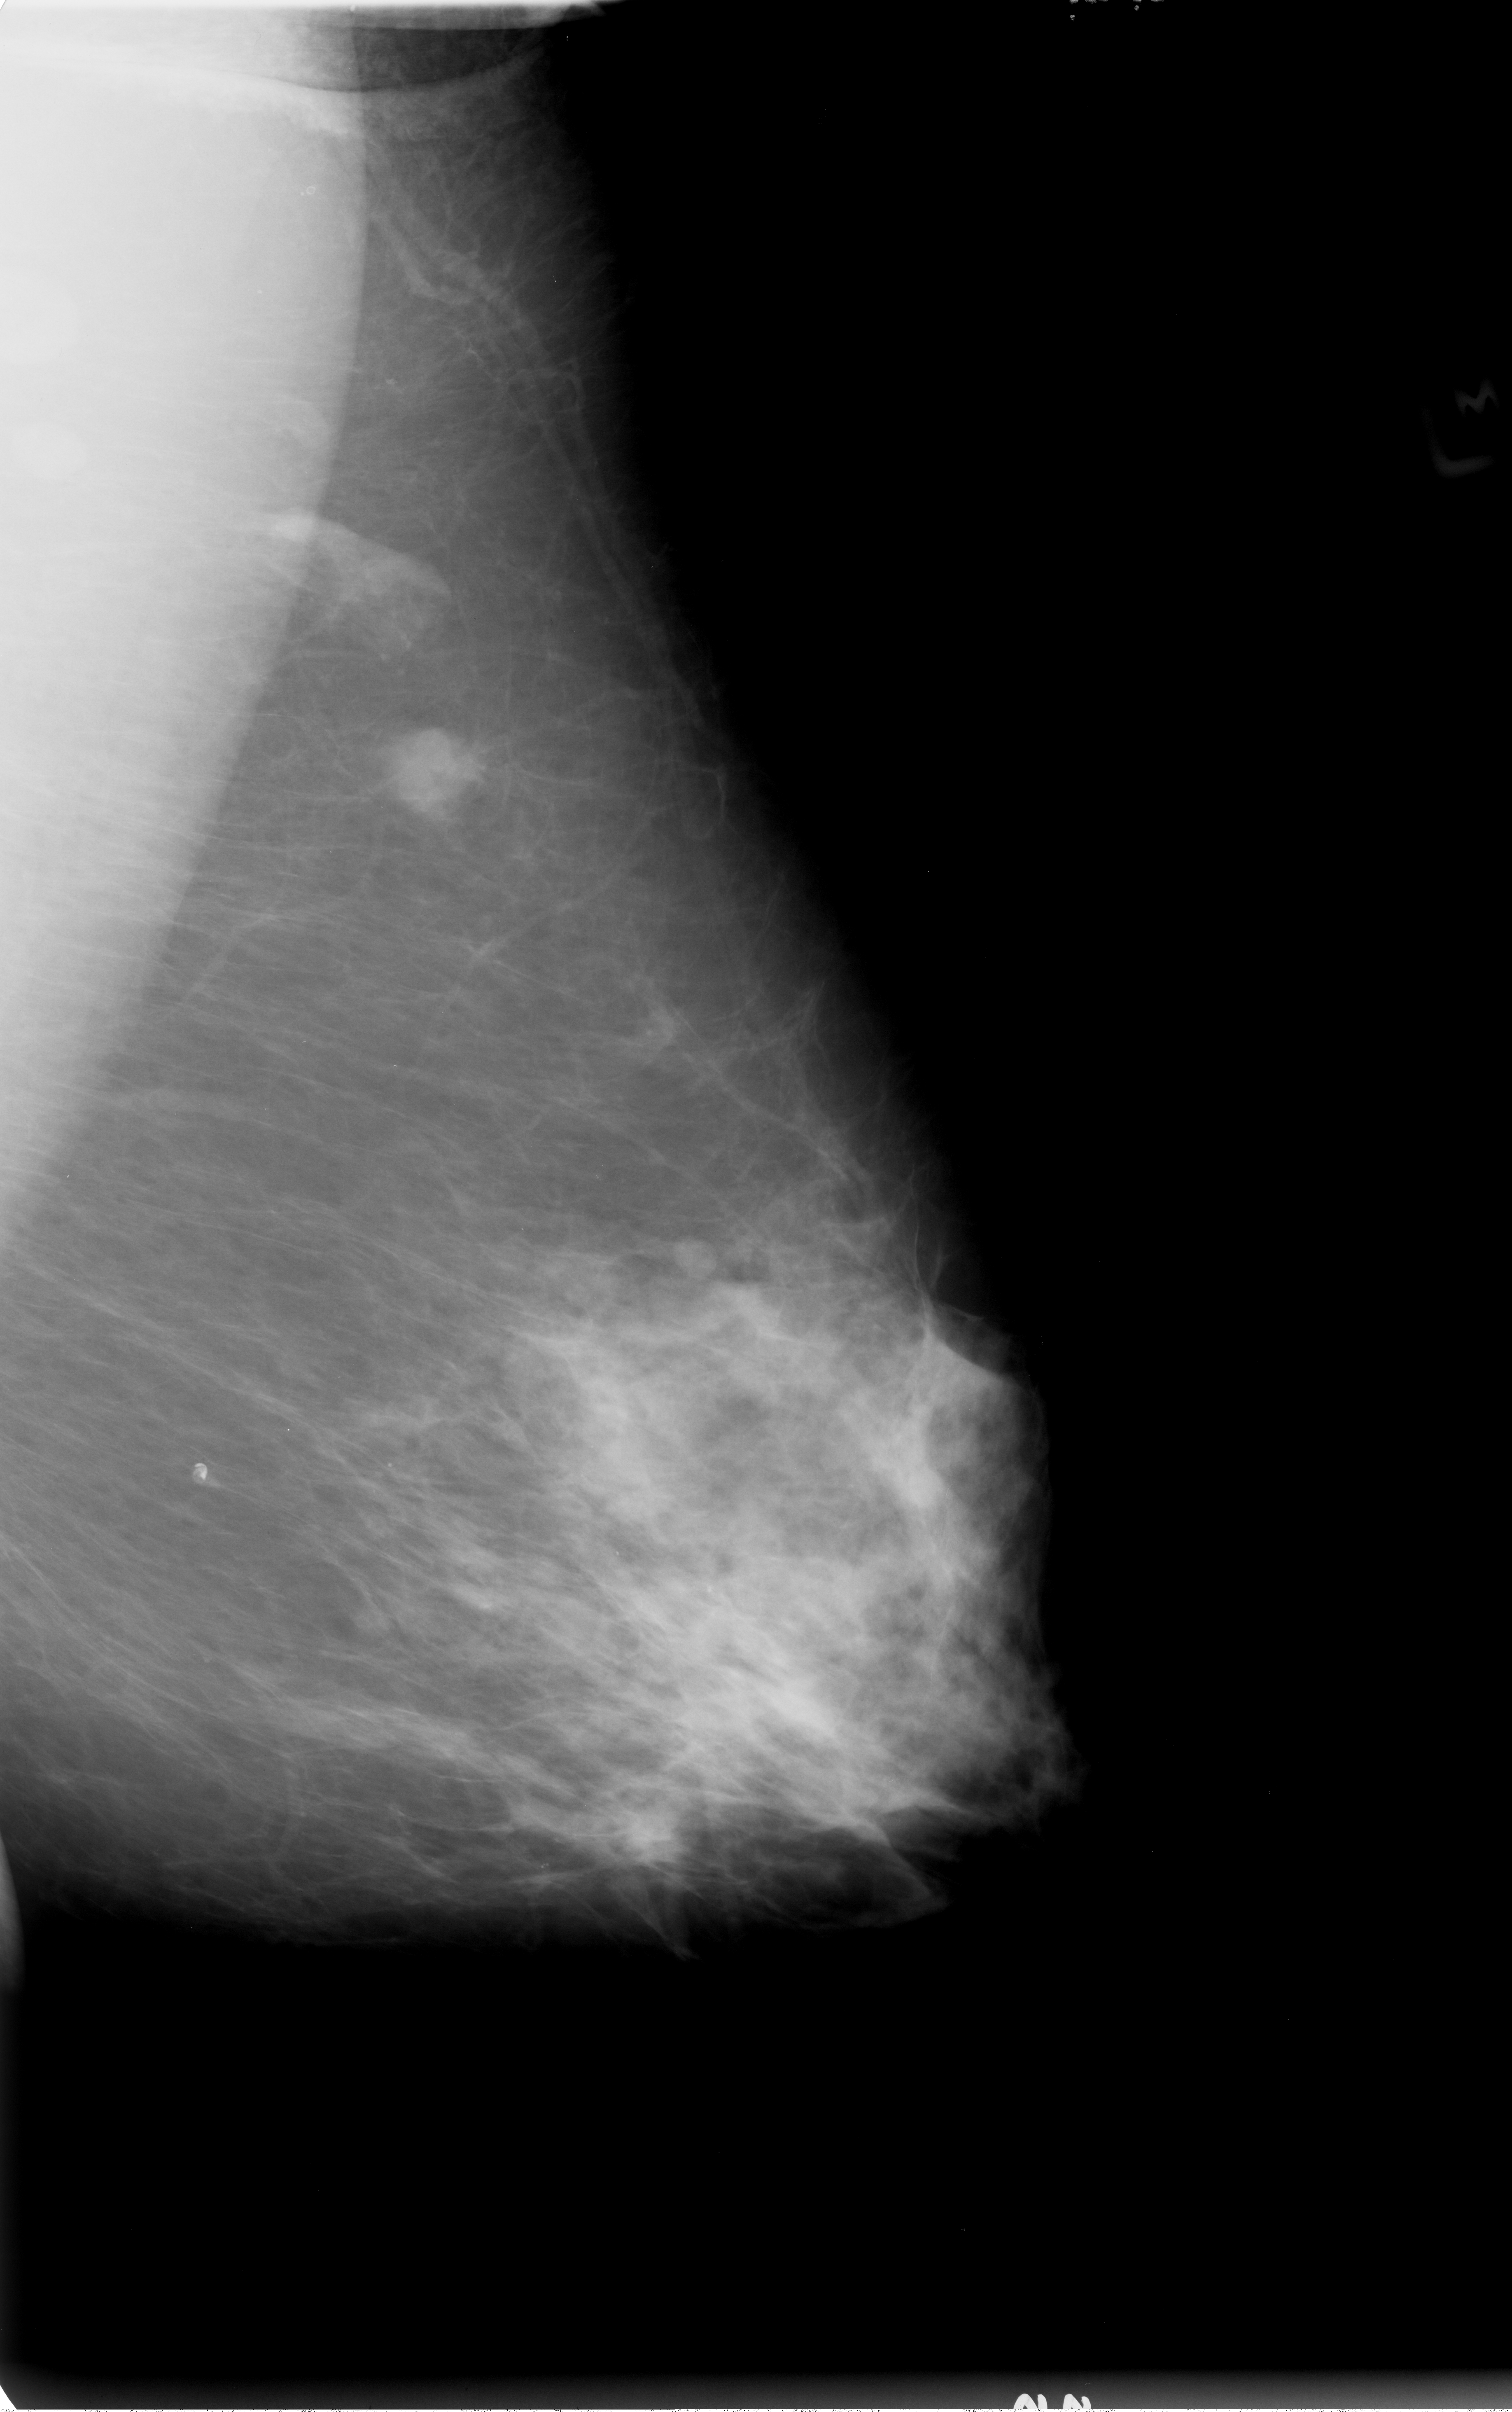
Digitized screen-film mammogram. Left breast. Mediolateral oblique (MLO) view. BI-RADS breast density category 3 (scale 1–4). 1512 × 2412 image matrix.
Marked abnormalities (boxes around the expert regions of interest):
- mass, shape lobulated / irregular, margins ill defined; BI-RADS assessment category 4; pathology (as recorded): malignant: bounding box <383,725,485,827> (left, top, right, bottom; pixels)